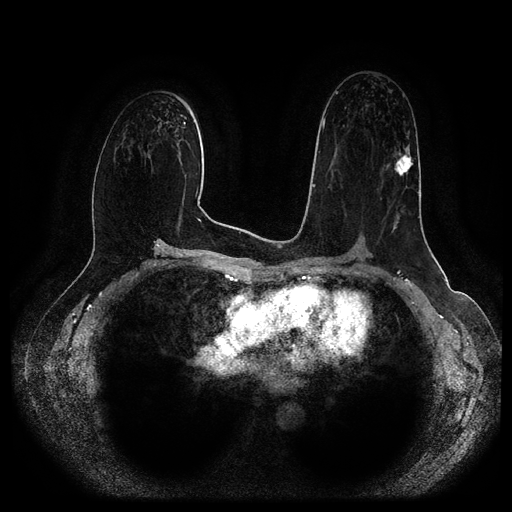
Breast MRI (dynamic contrast-enhanced, multi-phase), one axial slice. Position 58 of 116 along the scan axis. Dynamic contrast-enhanced series, time point 2 of 5 at this slice position (early post-contrast). 1.5 T. TE 2.6 ms, TR 5.2 ms. 2 mm slice thickness. 512 × 512 image matrix. Female patient, age 57 years.
Outlined on this slice (semi-automatically segmented with operator editing):
- breast lesion (labelled 'tumour' in the annotation; benign lesions carry a separate 'benign' label): bounding box [x1, y1, x2, y2] px = [394, 153, 414, 176]